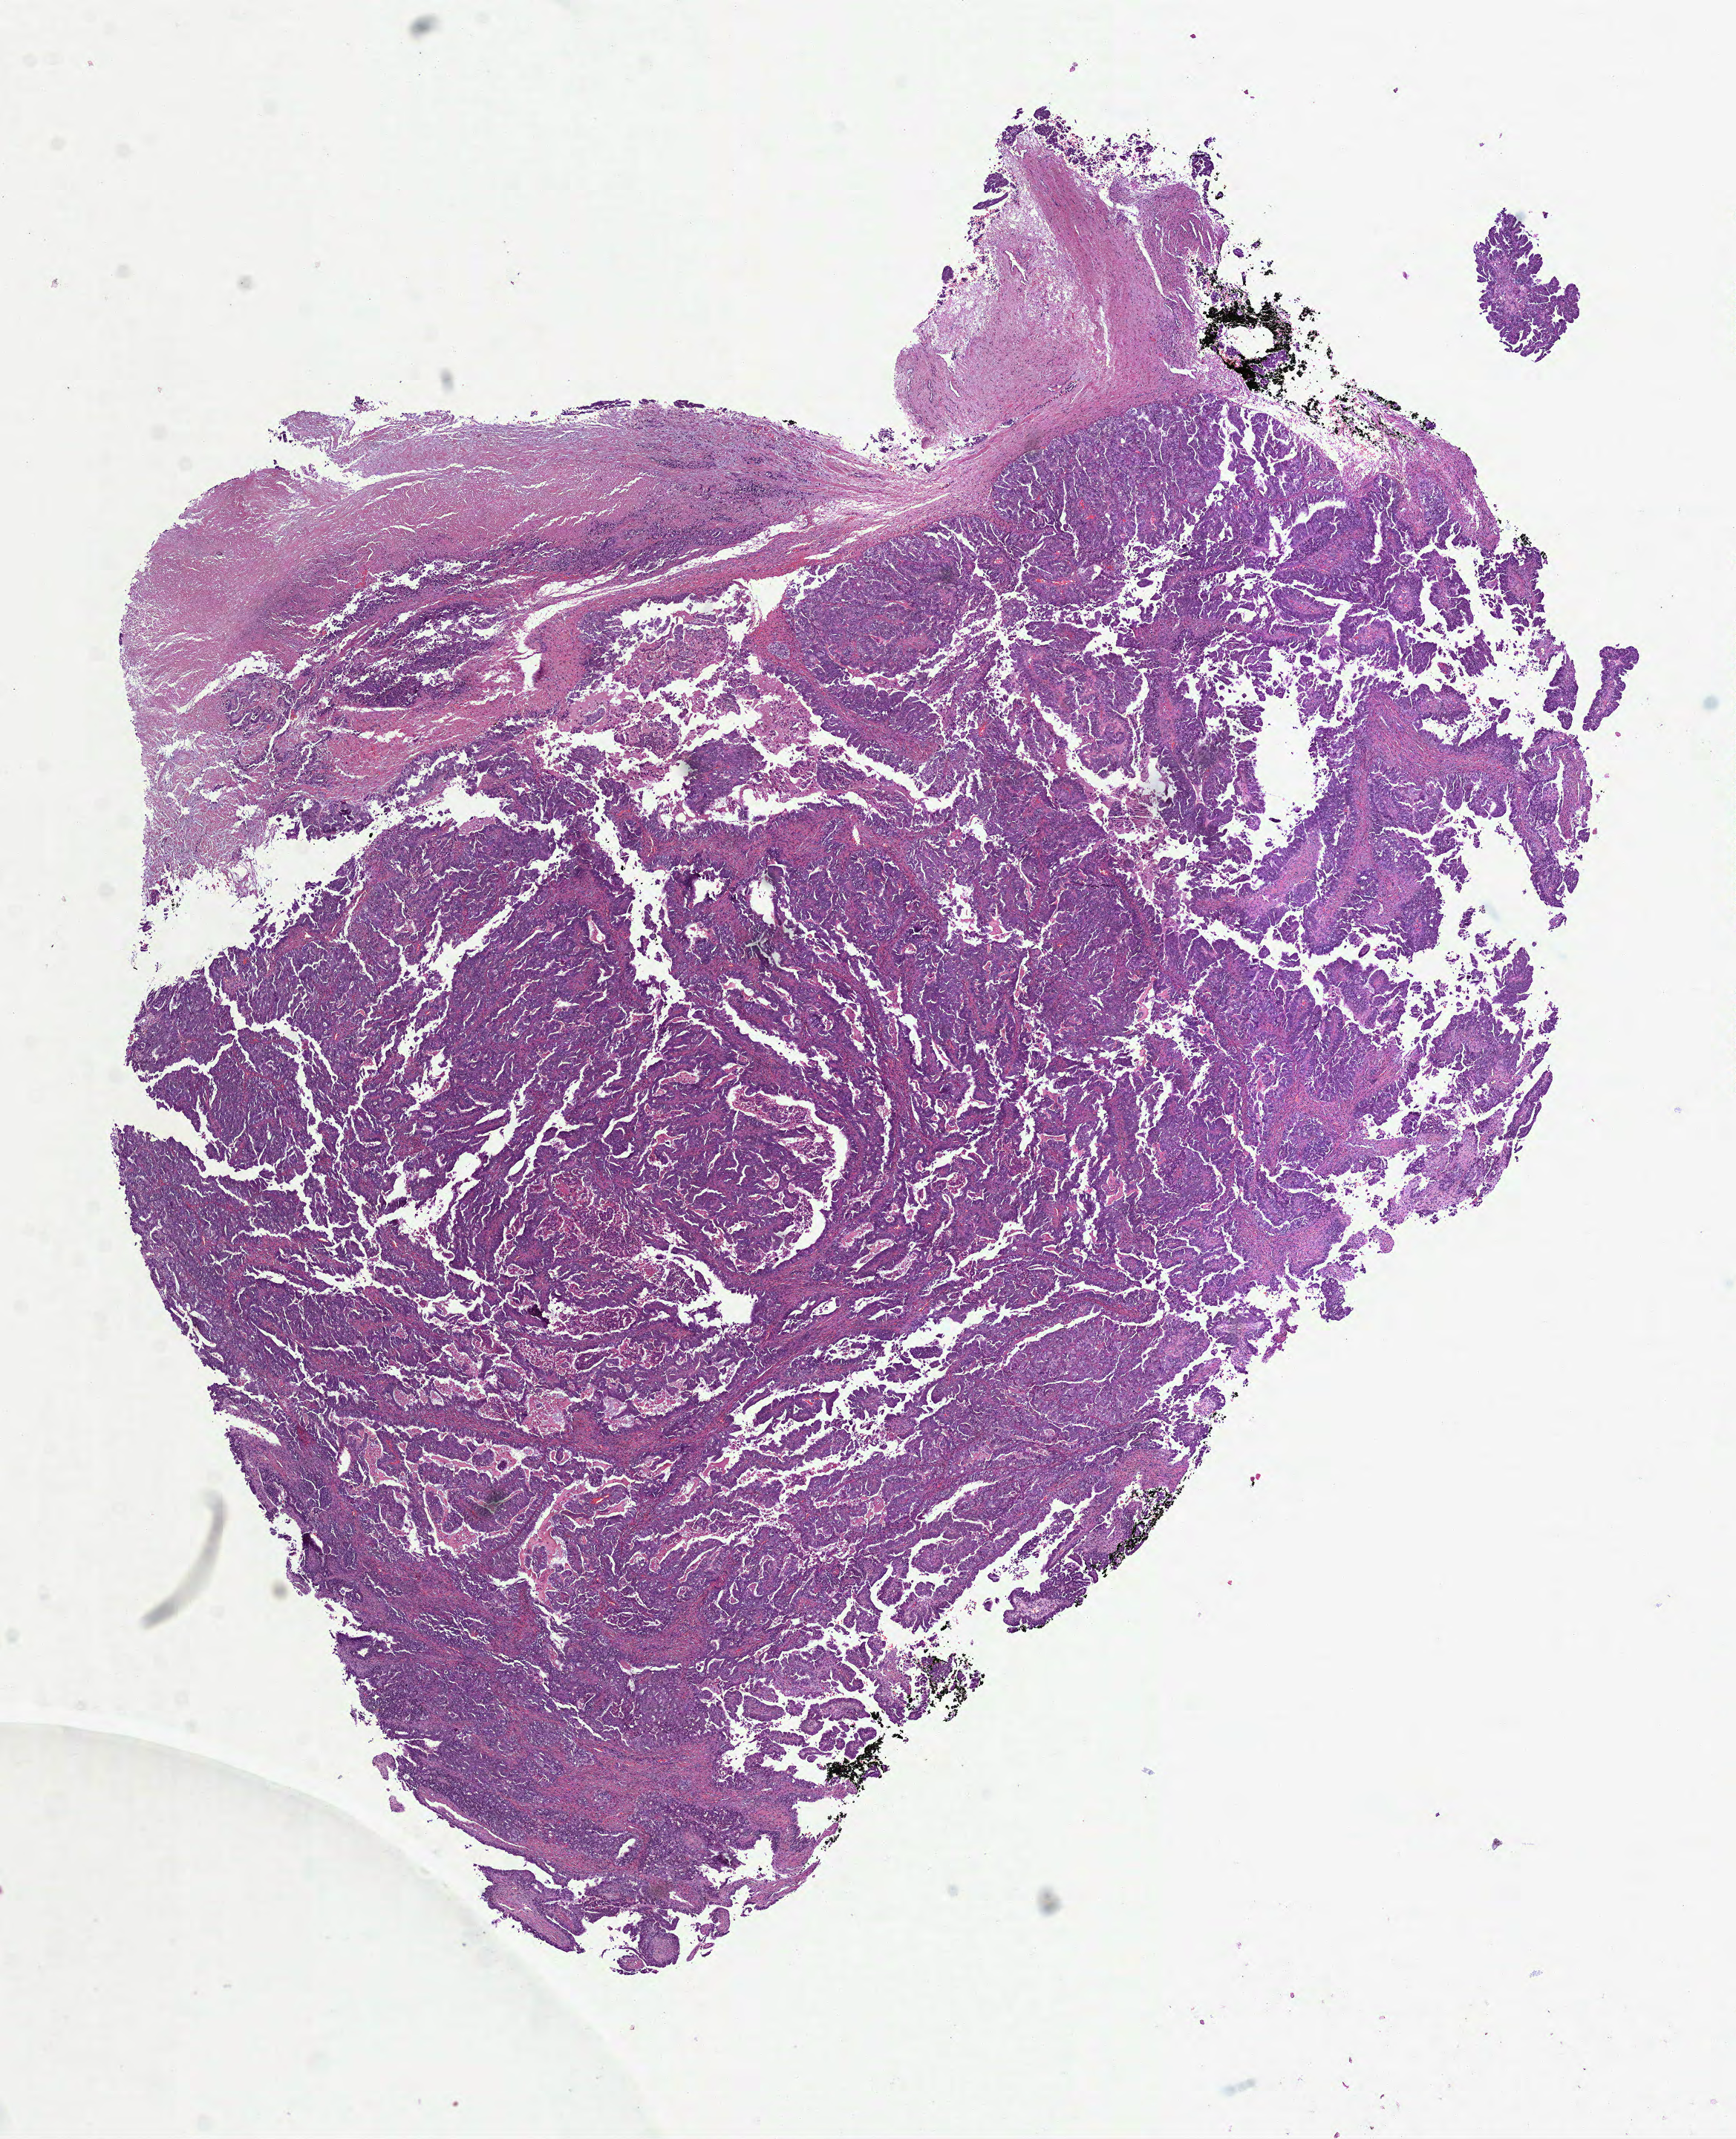
H&E-stained whole-slide image — low-resolution overview of the scanned area, about 9.4 x 11.6 mm (slide scanned at 40x), formalin-fixed paraffin-embedded (FFPE) diagnostic section, sample: primary tumour, ovary. Patient: female, age at initial diagnosis 66 years. Histologic grade: G3 (poorly differentiated).
Diagnosis: Serous cystadenocarcinoma, NOS. FIGO stage: IIIC.